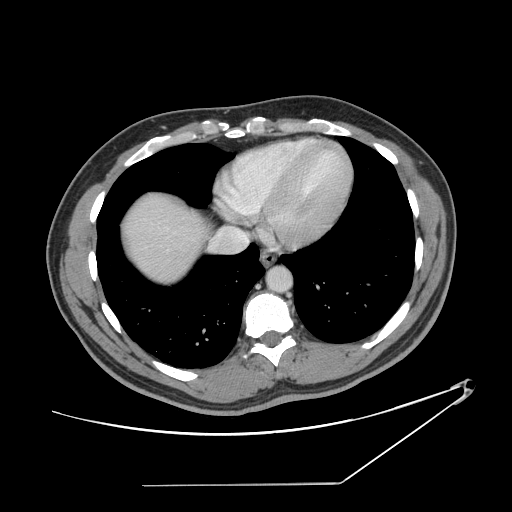
Contrast-enhanced abdominal CT, one axial slice. Slice 137 of 152 in the series (ordered by position). 120 kVp. Soft-tissue window (W 400 / L 40 HU). 2.5 mm slice thickness. 512 × 512 image matrix. Male patient, age 45 years. From the clinical record (not read from this slice): diagnosis: colorectal cancer liver metastases, imaged before liver resection; multiple liver metastases: no; largest metastasis: 1 cm; disease in both lobes: no.
Structures marked on this image (manually delineated by an expert):
- hepatic veins: box from (x=229, y=229) to (x=248, y=244) px
- liver: (x=125, y=194)–(x=205, y=282)
- planned liver remnant (the part of the liver to remain after resection): (x=125, y=194)–(x=204, y=282)